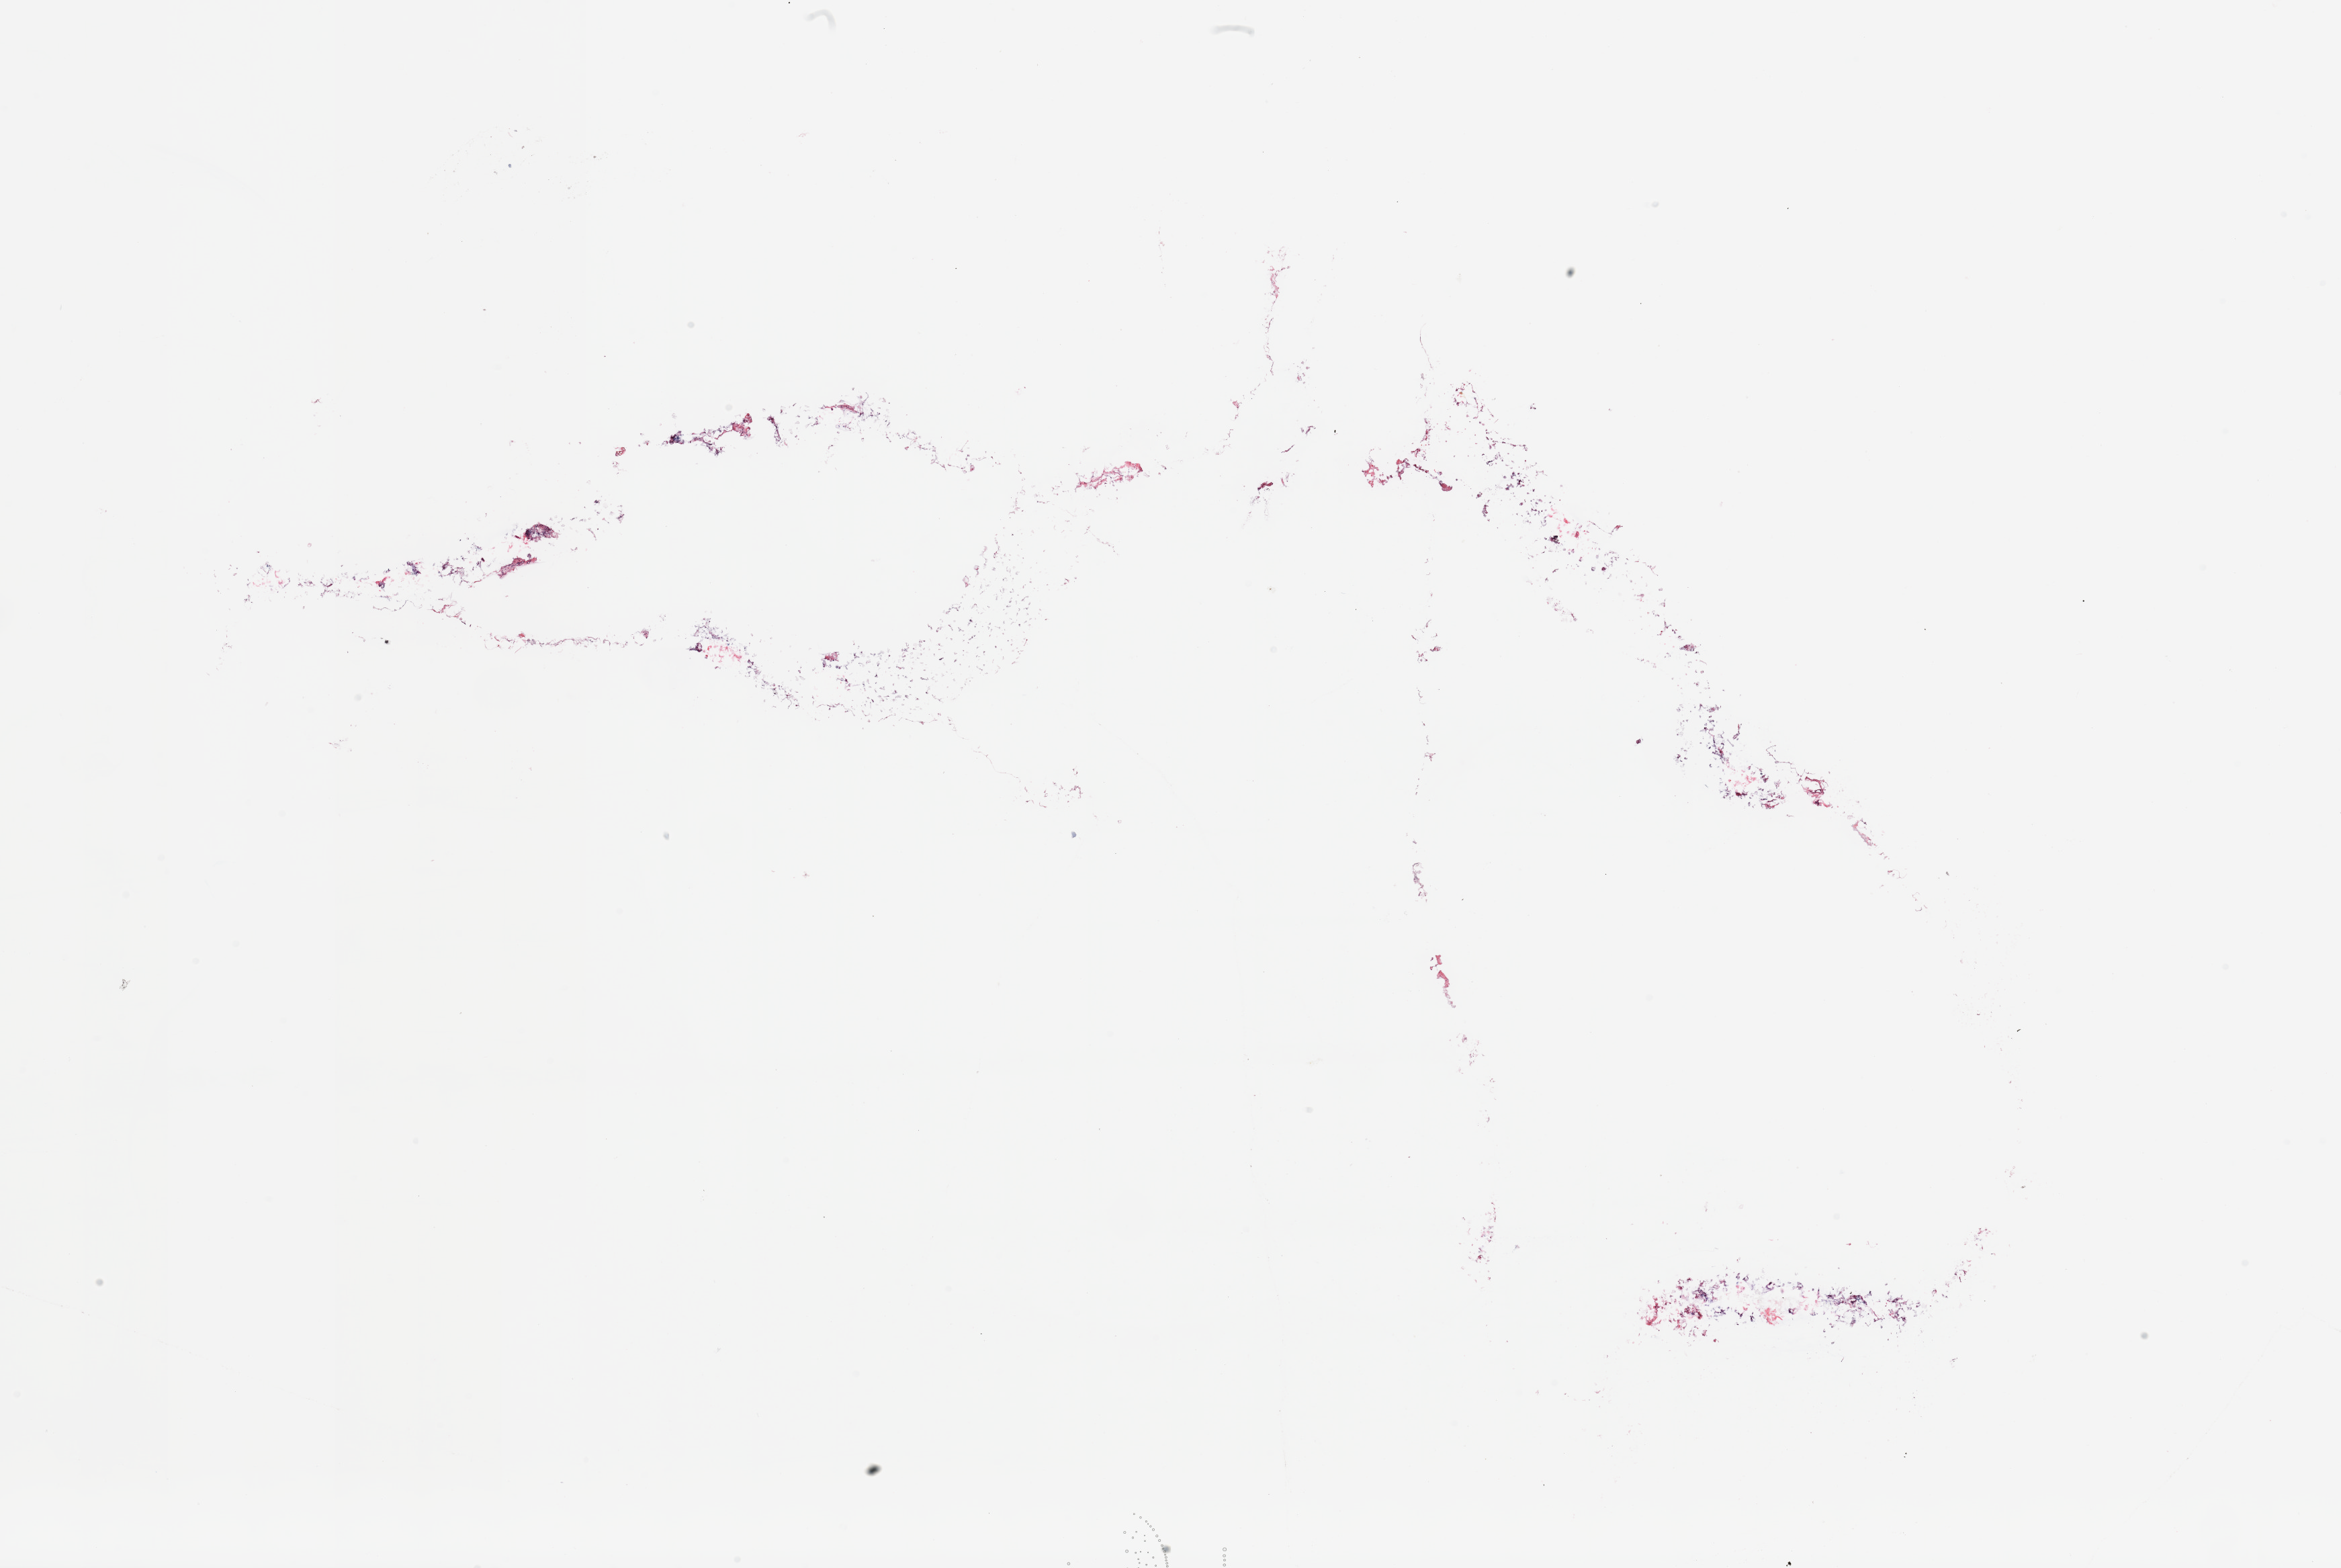
Digitized H&E tissue section (whole slide) — low-resolution overview of the scanned area, about 27.6 x 18.5 mm (acquisition: 20x scan), breast, tumour tissue. 50-year-old female patient.
* AJCC pathologic stage: IIB
* histologic diagnosis: Infiltrating duct carcinoma, NOS